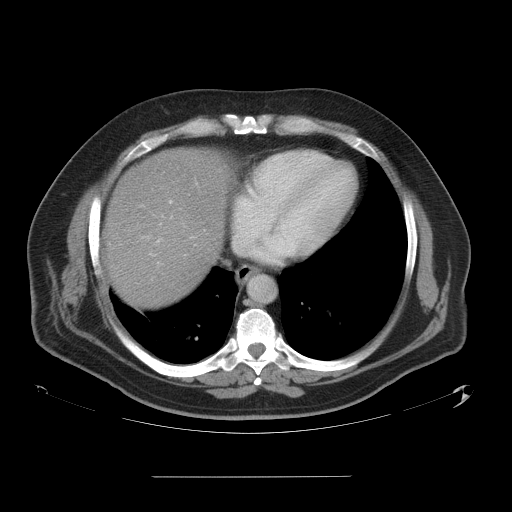
Contrast-enhanced abdominal CT, one axial slice. Slice 51 of 58 in the series (ordered by position). 120 kVp. Intravenous contrast given. Soft-tissue window (W 400 / L 40 HU). 5 mm slice thickness. 512 × 512 image matrix. Male patient, age 63 years. From the clinical record (not read from this slice): diagnosis: colorectal cancer liver metastases, imaged before liver resection; multiple liver metastases: no; largest metastasis: 4.2 cm; disease in both lobes: no.
Structures marked on this image (outlined manually by an expert reader):
- hepatic veins: bounding box [x1, y1, x2, y2] px = [155, 183, 246, 256]
- liver: [107, 149, 230, 307]
- planned liver remnant (the part of the liver to remain after resection): [107, 213, 215, 307]
- portal vein (with intrahepatic branches): [150, 200, 172, 257]